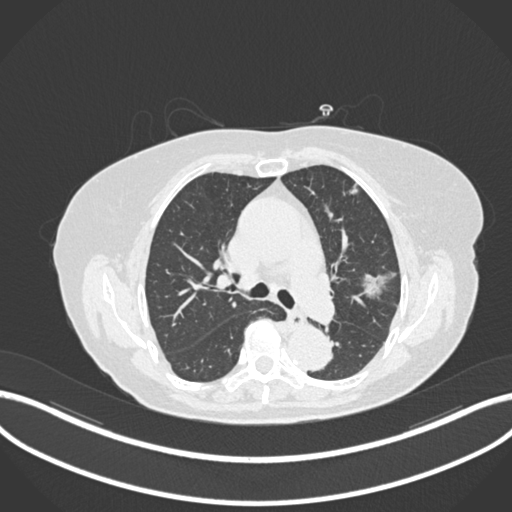
Chest CT, one axial slice; slice 101 of 168 in the series (ordered by position); 120 kVp; lung window (W 1500 / L -600 HU); 1 mm slice thickness; 512 × 512 image matrix. Patient: female, 75 years. From the clinical record (not read from this slice): clinical TNM (as recorded): T1c N0 M0.
Outlined on this slice (bounding box drawn by a radiologist):
- lung tumour (recorded histology: adenocarcinoma): bounding box [x1, y1, x2, y2] px = [361, 270, 396, 300]